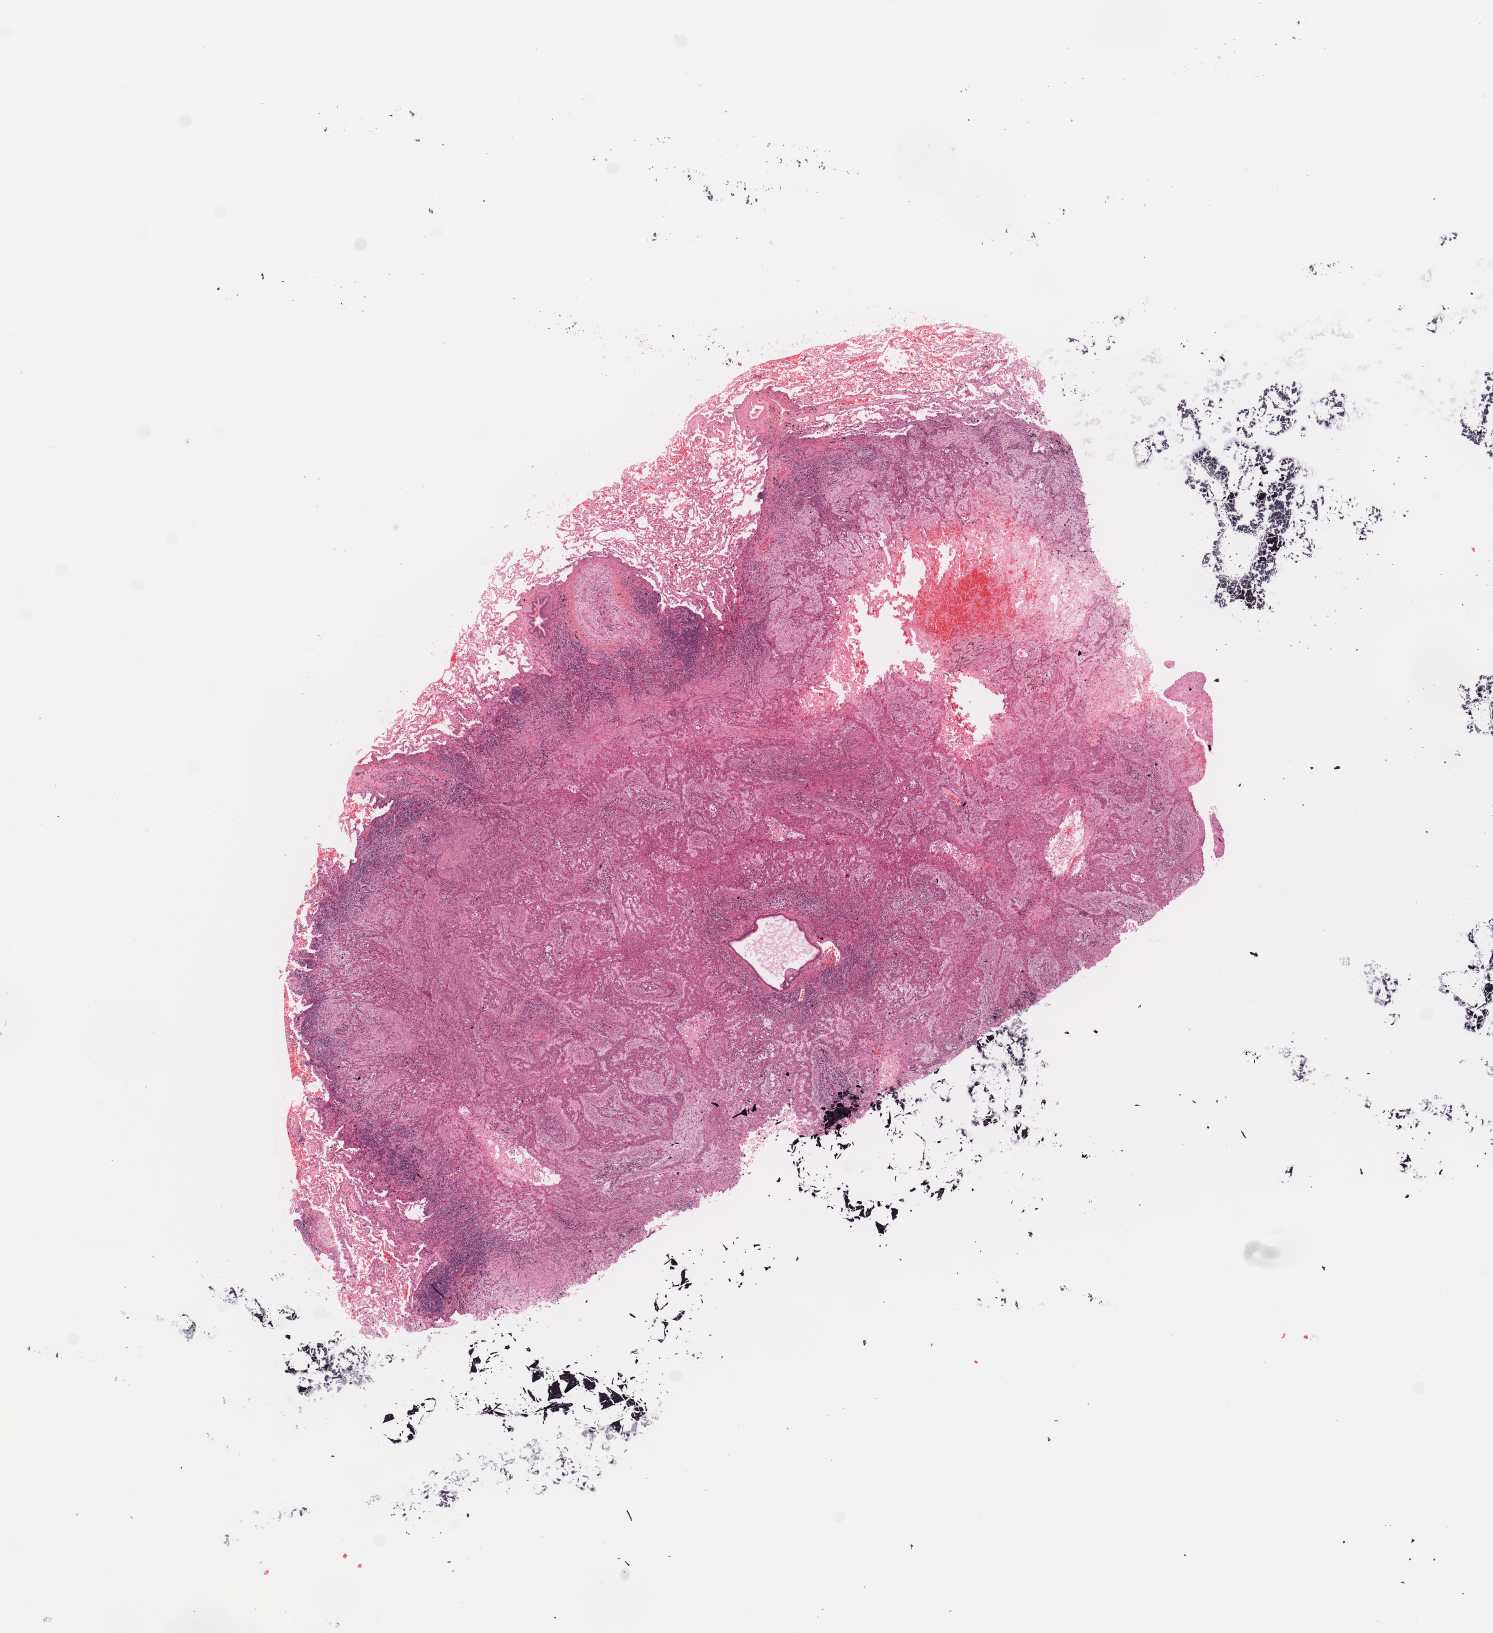
Digitized H&E-stained tissue section (whole slide) — a low-resolution overview of the entire scanned area, about 11.8 x 12.9 mm (from a 20x scan); tumour tissue sample, sampled site: lung. 69-year-old female patient. Histologic grade: G3 (poorly differentiated). Pathologist review of this section (percent, as recorded): tumour nuclei 70%, necrosis 5%.
AJCC pathologic stage: IA. Primary tumour site (as recorded): right lower lobe. Diagnosis: Squamous cell carcinoma, NOS.